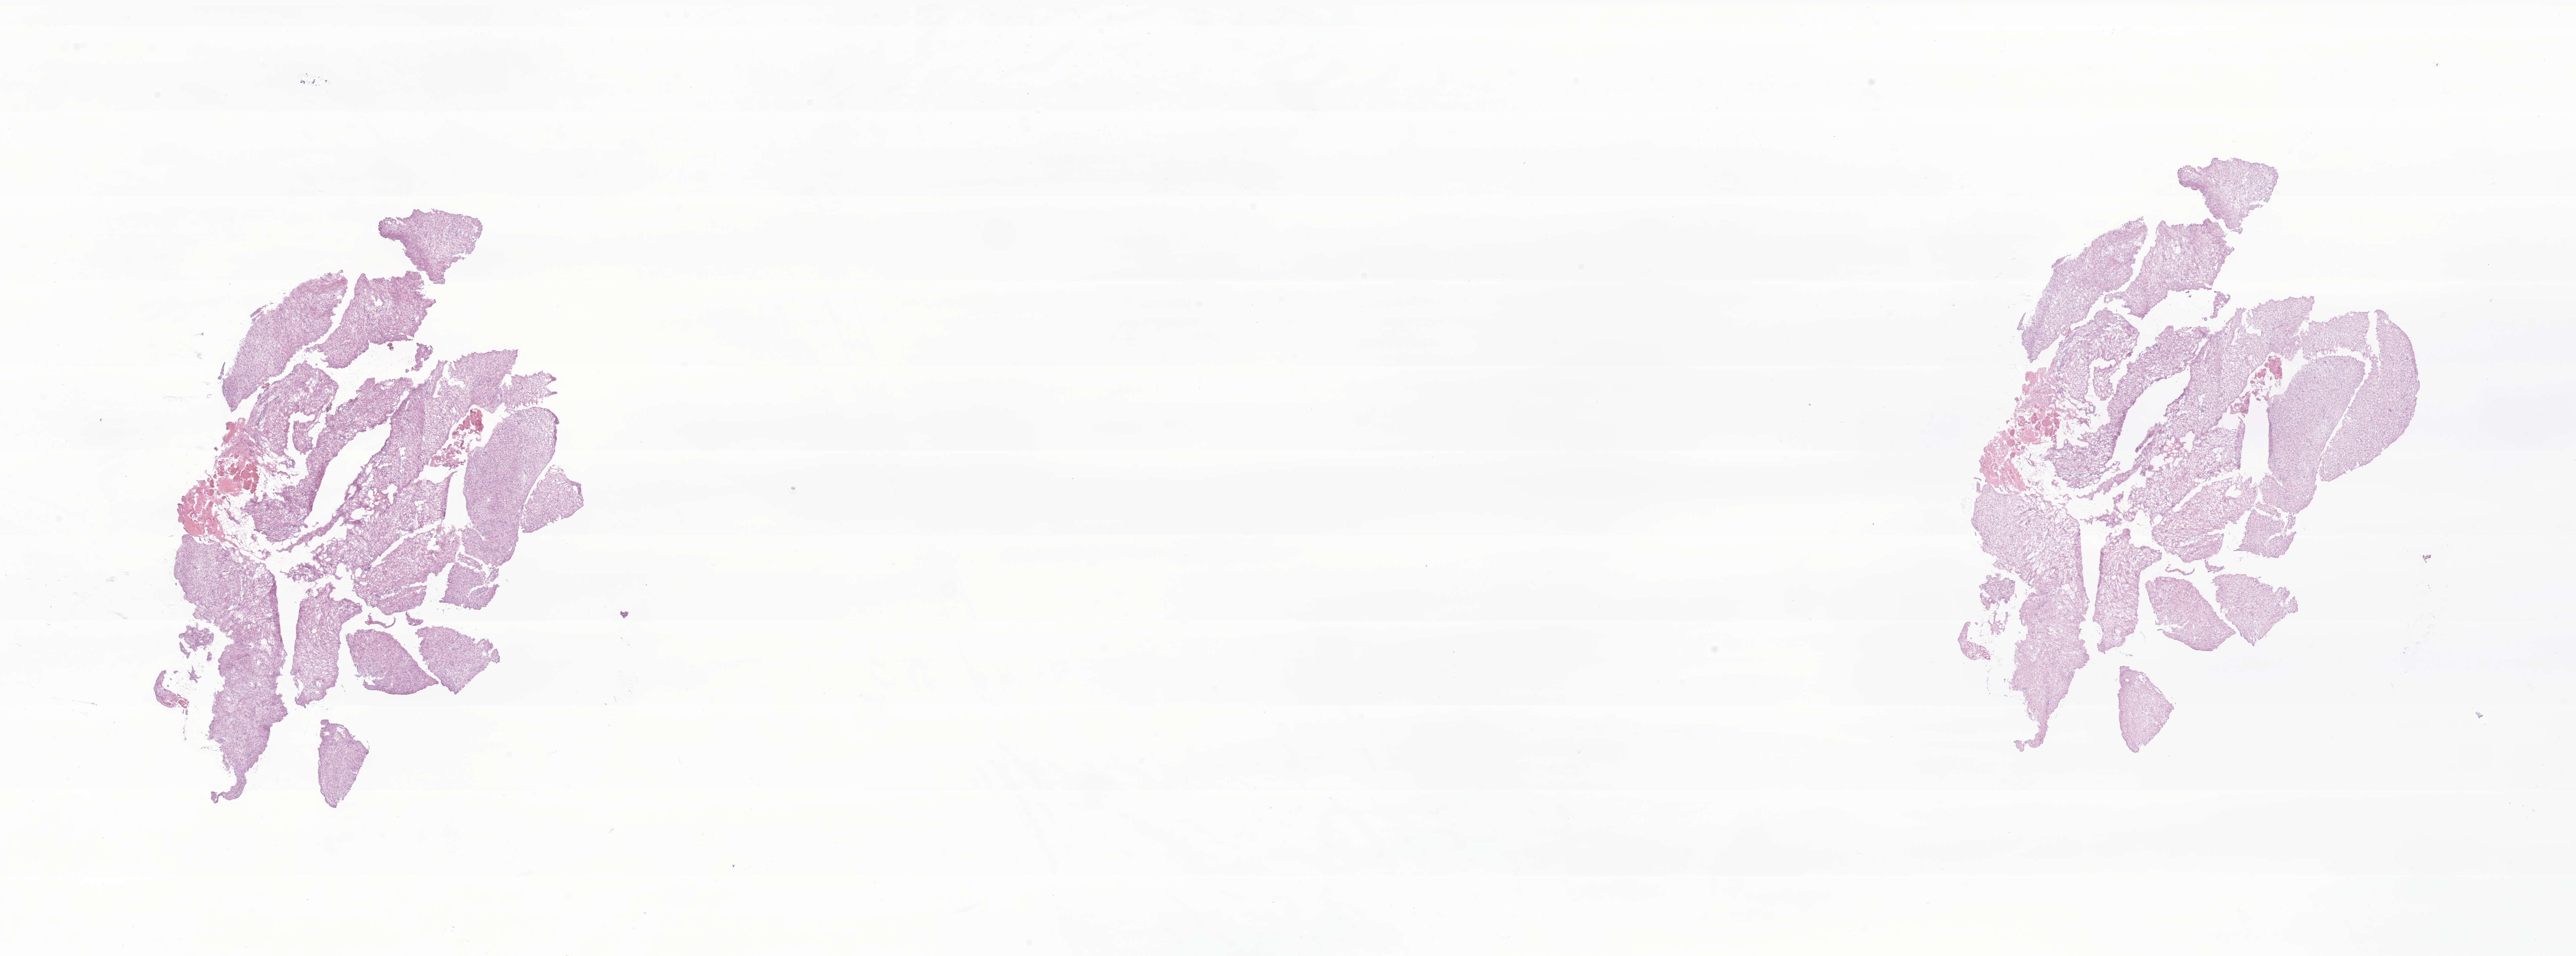
Digitized haematoxylin and eosin-stained section of tumor tissue from the soft tissue of thorax — whole scanned area (about 32.4 x 12.0 mm) shown as a low-resolution overview; frozen section (OCT-embedded). Male patient, age 183 months (15 years 3 months).
Tissue or organ of origin (case record): connective, subcutaneous and other soft tissues of thorax. Recorded diagnosis: Sarcoma, NOS.